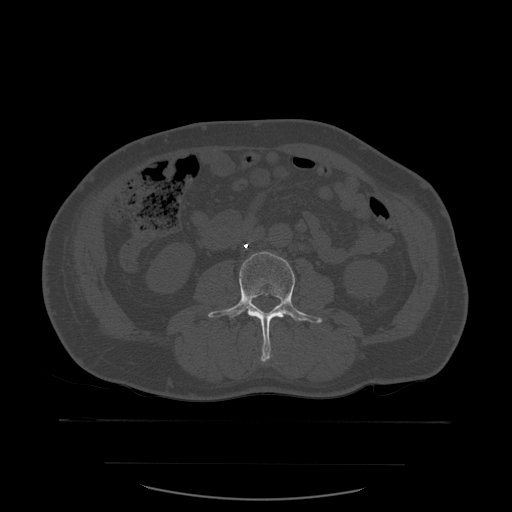
CT including the spine, one axial slice. Bone window (W 1800 / L 400 HU). 1.25 mm slice thickness. 512 × 512 image matrix, field of view 479 × 479 mm. Patient age 71 years. Case-level facts recorded for this patient, not image findings: primary cancer: lung.
Annotated regions visible in this slice (semi-automatic segmentation, software-assisted and operator-edited):
- L3 vertebra: box from (x=208, y=252) to (x=323, y=362) px